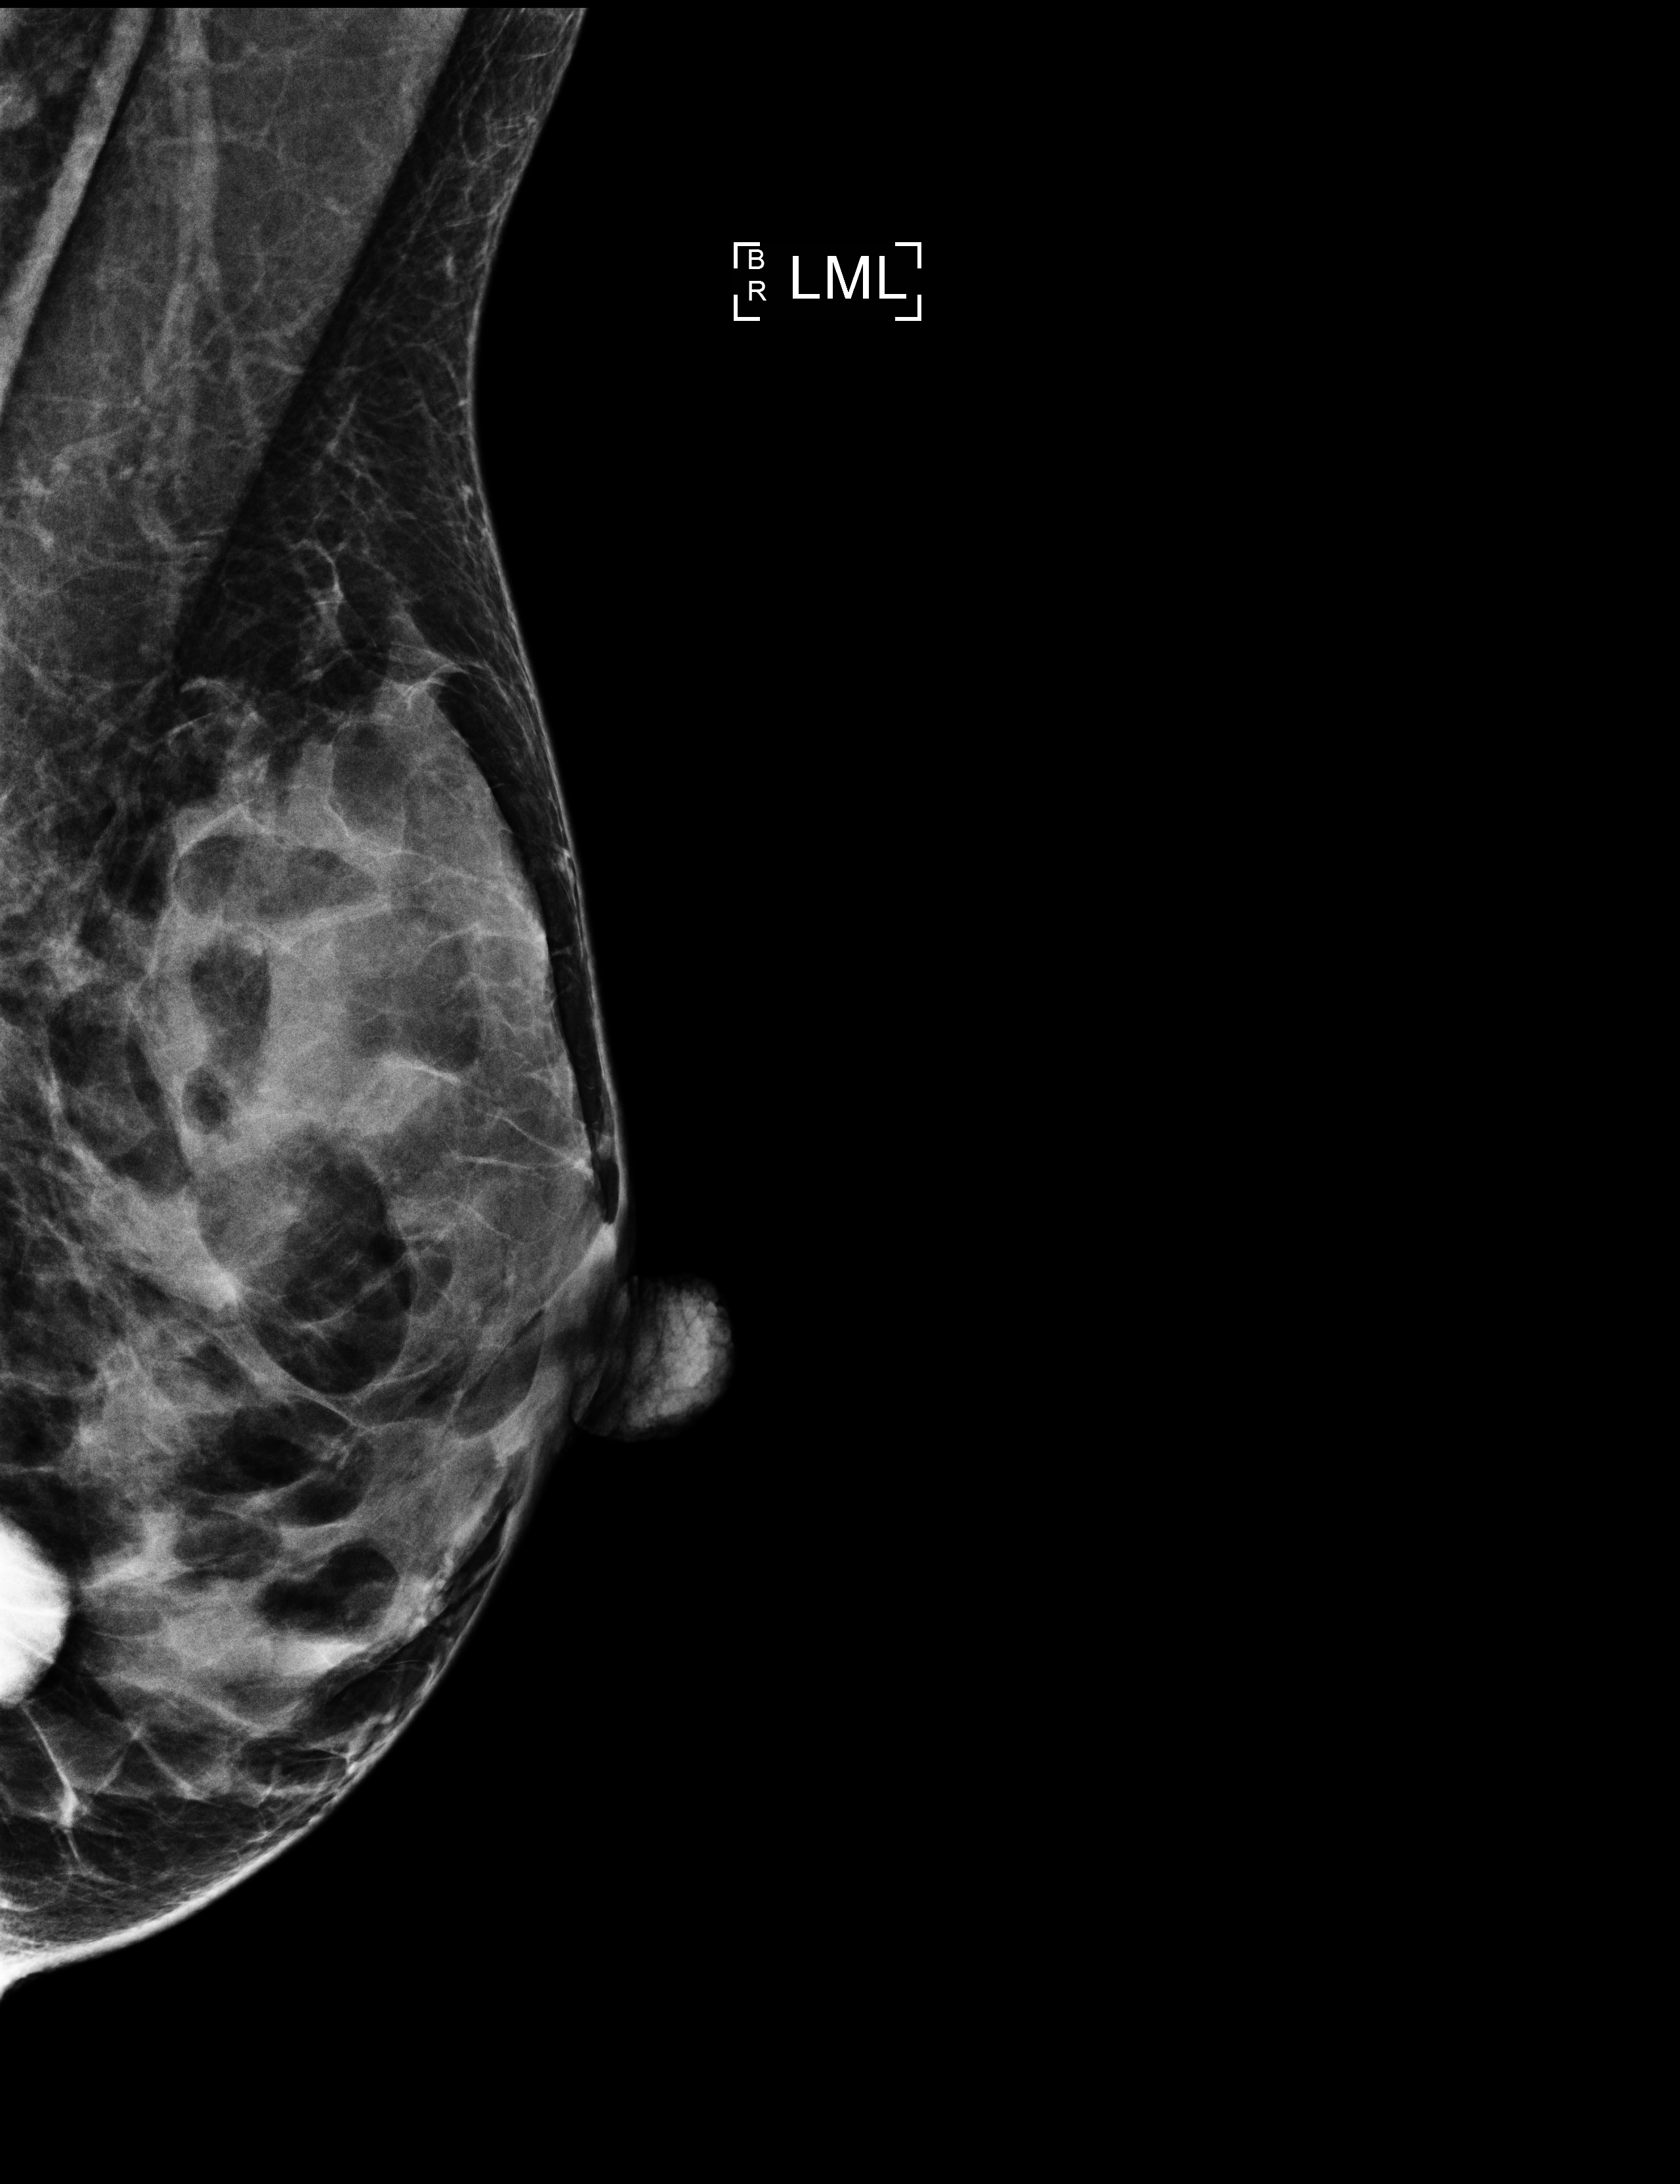
Digital mammogram (FFDM), left breast, mediolateral (ML) view, diagnostic examination (additional views). Female patient, age 42 years.
- BI-RADS breast density category at the screening exam (both breasts, scale 1–4): 4
- final BI-RADS assessment for this screening round (tomosynthesis exam, both breasts): category 2
- recall: recalled for additional imaging after this screen